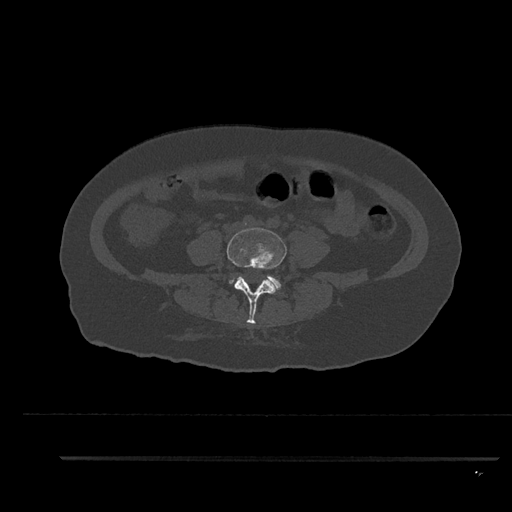
CT including the spine, one axial slice. Position 4 of 797 along the scan axis. Reconstruction kernel Br40s/3. 120 kVp. Bone window (W 1800 / L 400 HU). 512 × 512 image matrix, field of view 408 × 408 mm. Patient: female, 44 years. Case-level facts recorded for this patient, not image findings: primary cancer: renal; vertebrae with lytic lesions (as recorded): L1.
Outlined on this slice (semi-automatically segmented with operator editing):
- L4 vertebra: bounding box [x1, y1, x2, y2] px = [227, 228, 287, 324]